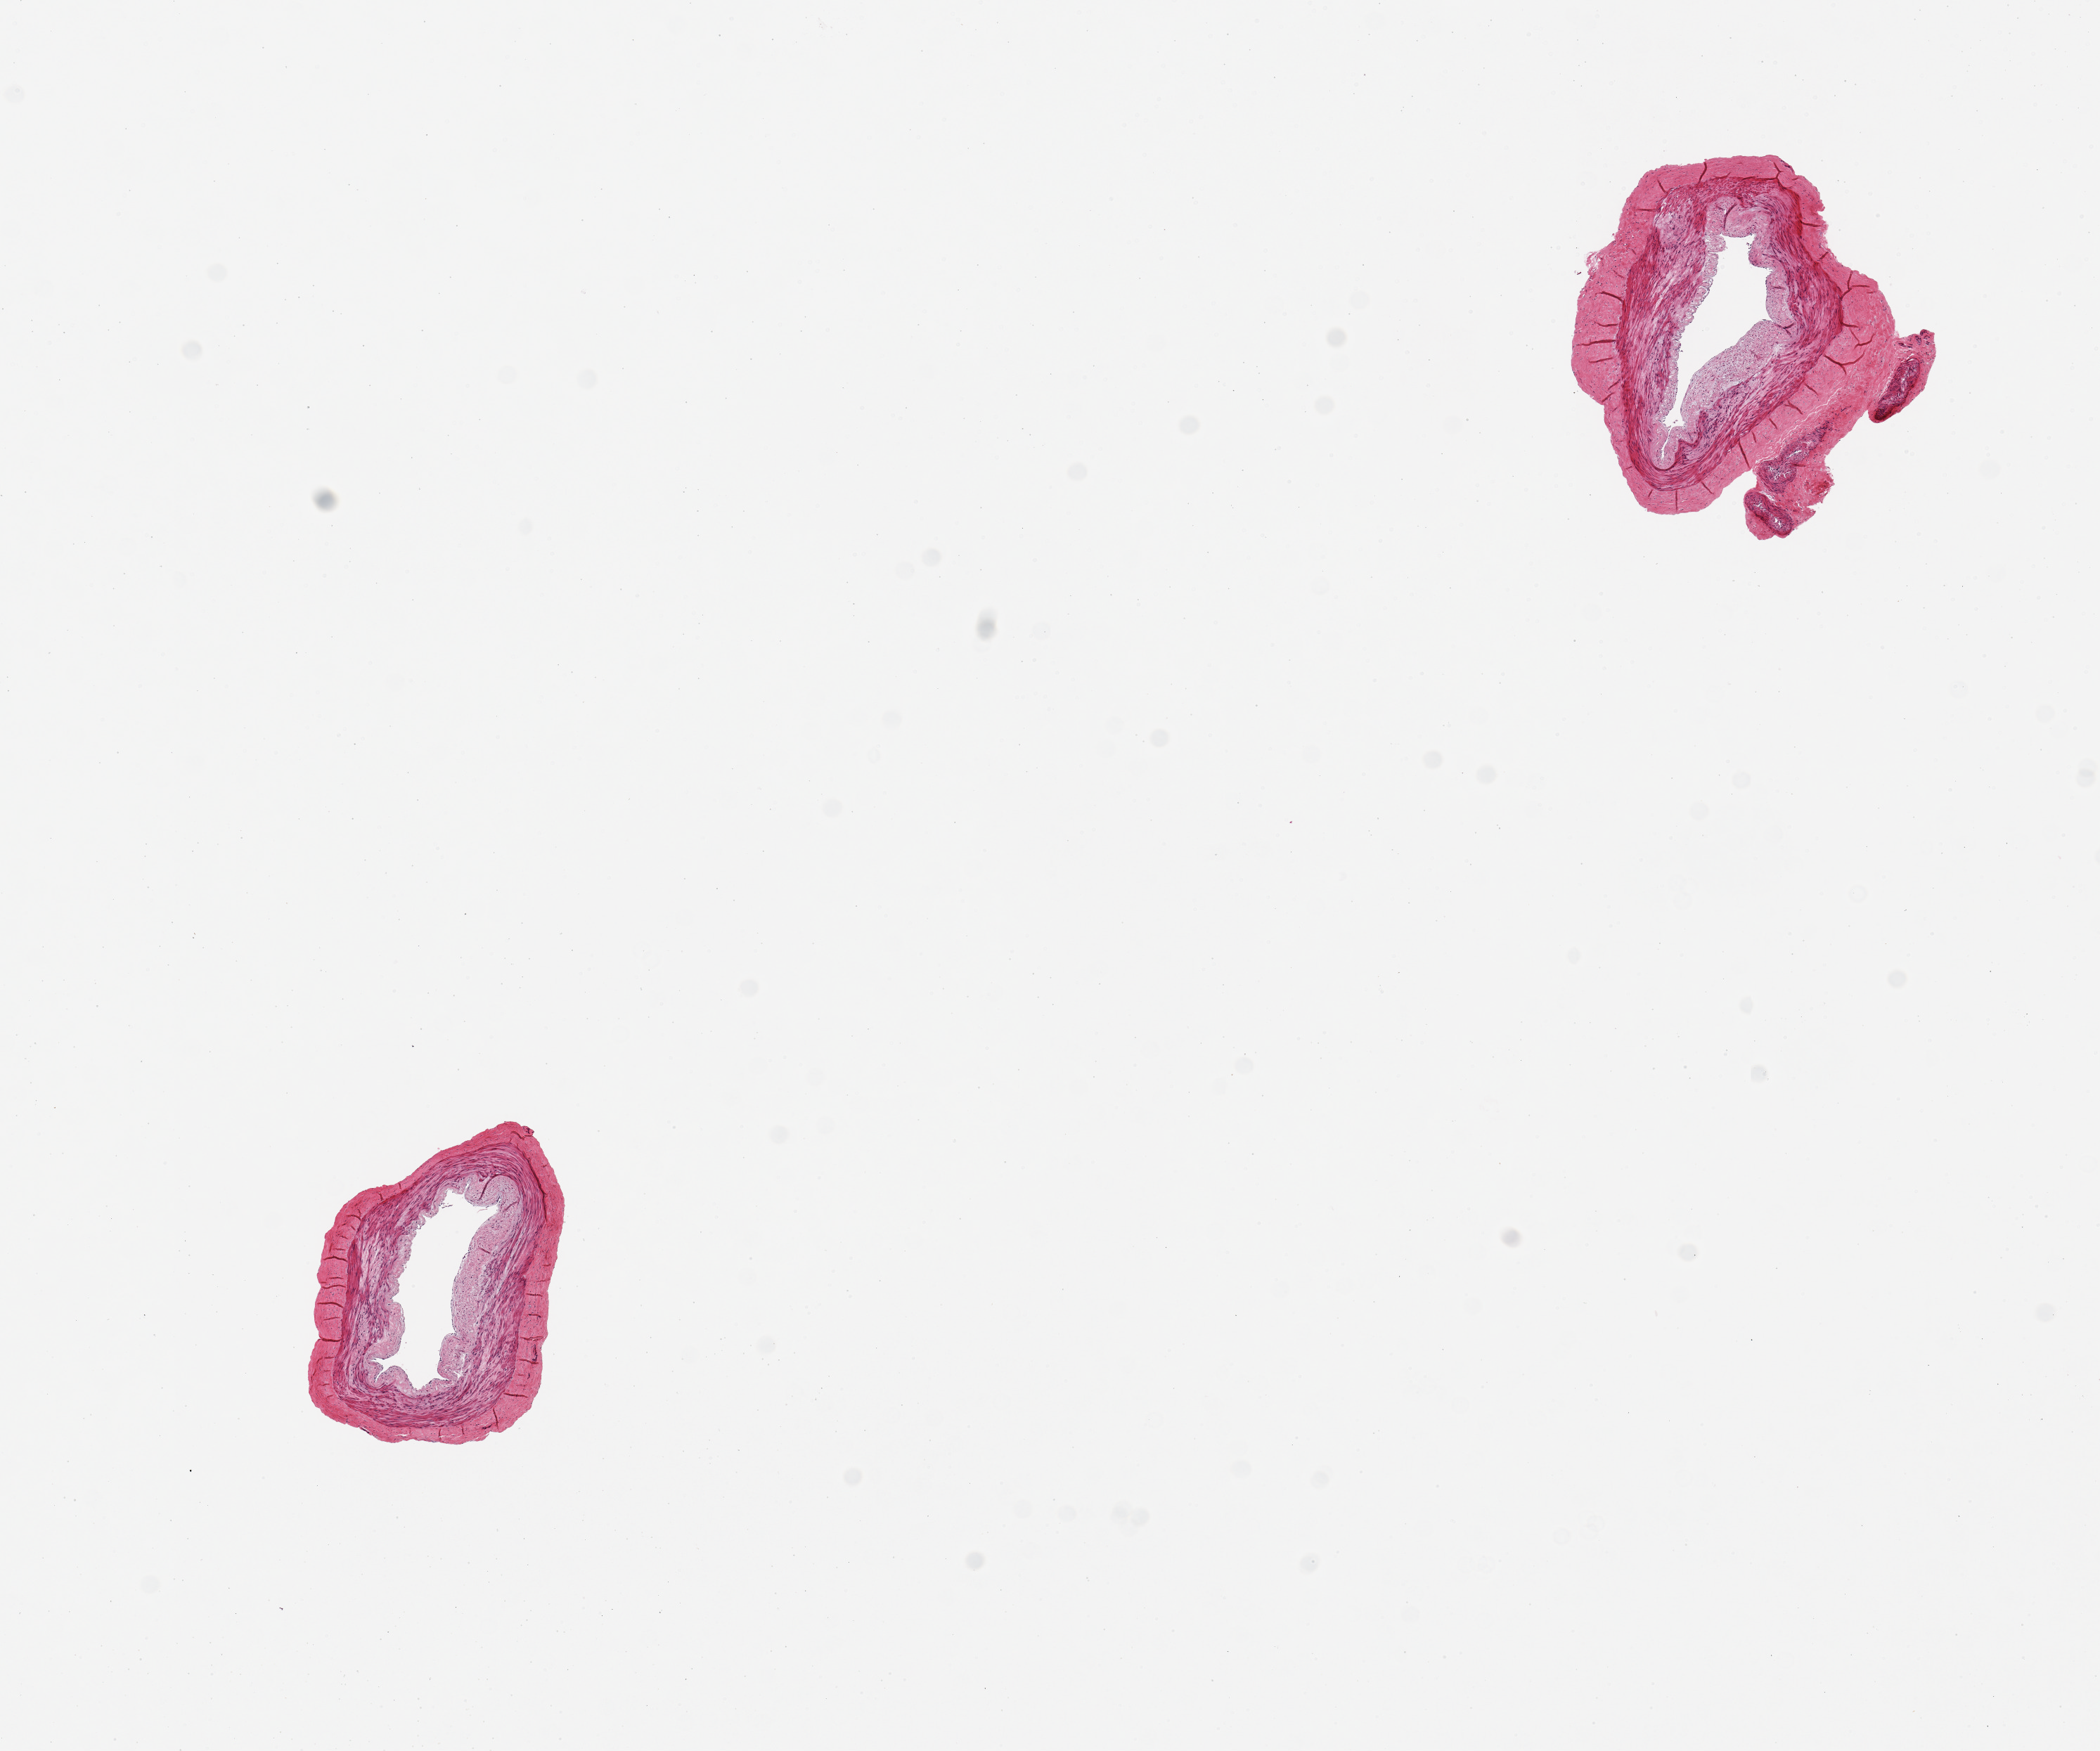
Digitized haematoxylin and eosin-stained section — shown as a low-resolution overview of the whole scanned area (about 11.8 x 9.9 mm, acquisition: 20x scan); PAXgene-fixed, paraffin-embedded tissue; sampled site (target tissue): tibial artery; tissue donor sample. Donor: female.
Reviewer comment on this tissue sample: 2 pieces, 2x1 & 2x2mm; small nubbin of ahderent smaller vessels in one sectoin.